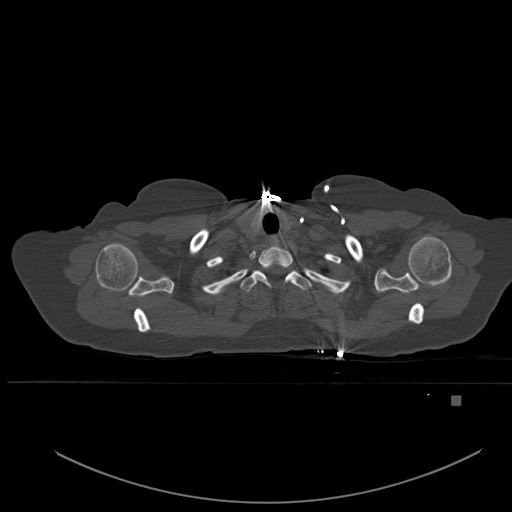
CT including the spine, one axial slice; slice 423 of 651 in the series (ordered by position); bone window (W 1800 / L 400 HU); 512 × 512 image matrix, field of view 443 × 443 mm. Patient: female, 49 years. From the clinical record (not read from this slice): primary cancer: breast; vertebrae with lytic lesions (as recorded): L3, T12, L4.
Outlined on this slice (semi-automatic segmentation, software-assisted and operator-edited):
- T1 vertebra: bounding box <240,270,312,292> (left, top, right, bottom; pixels)